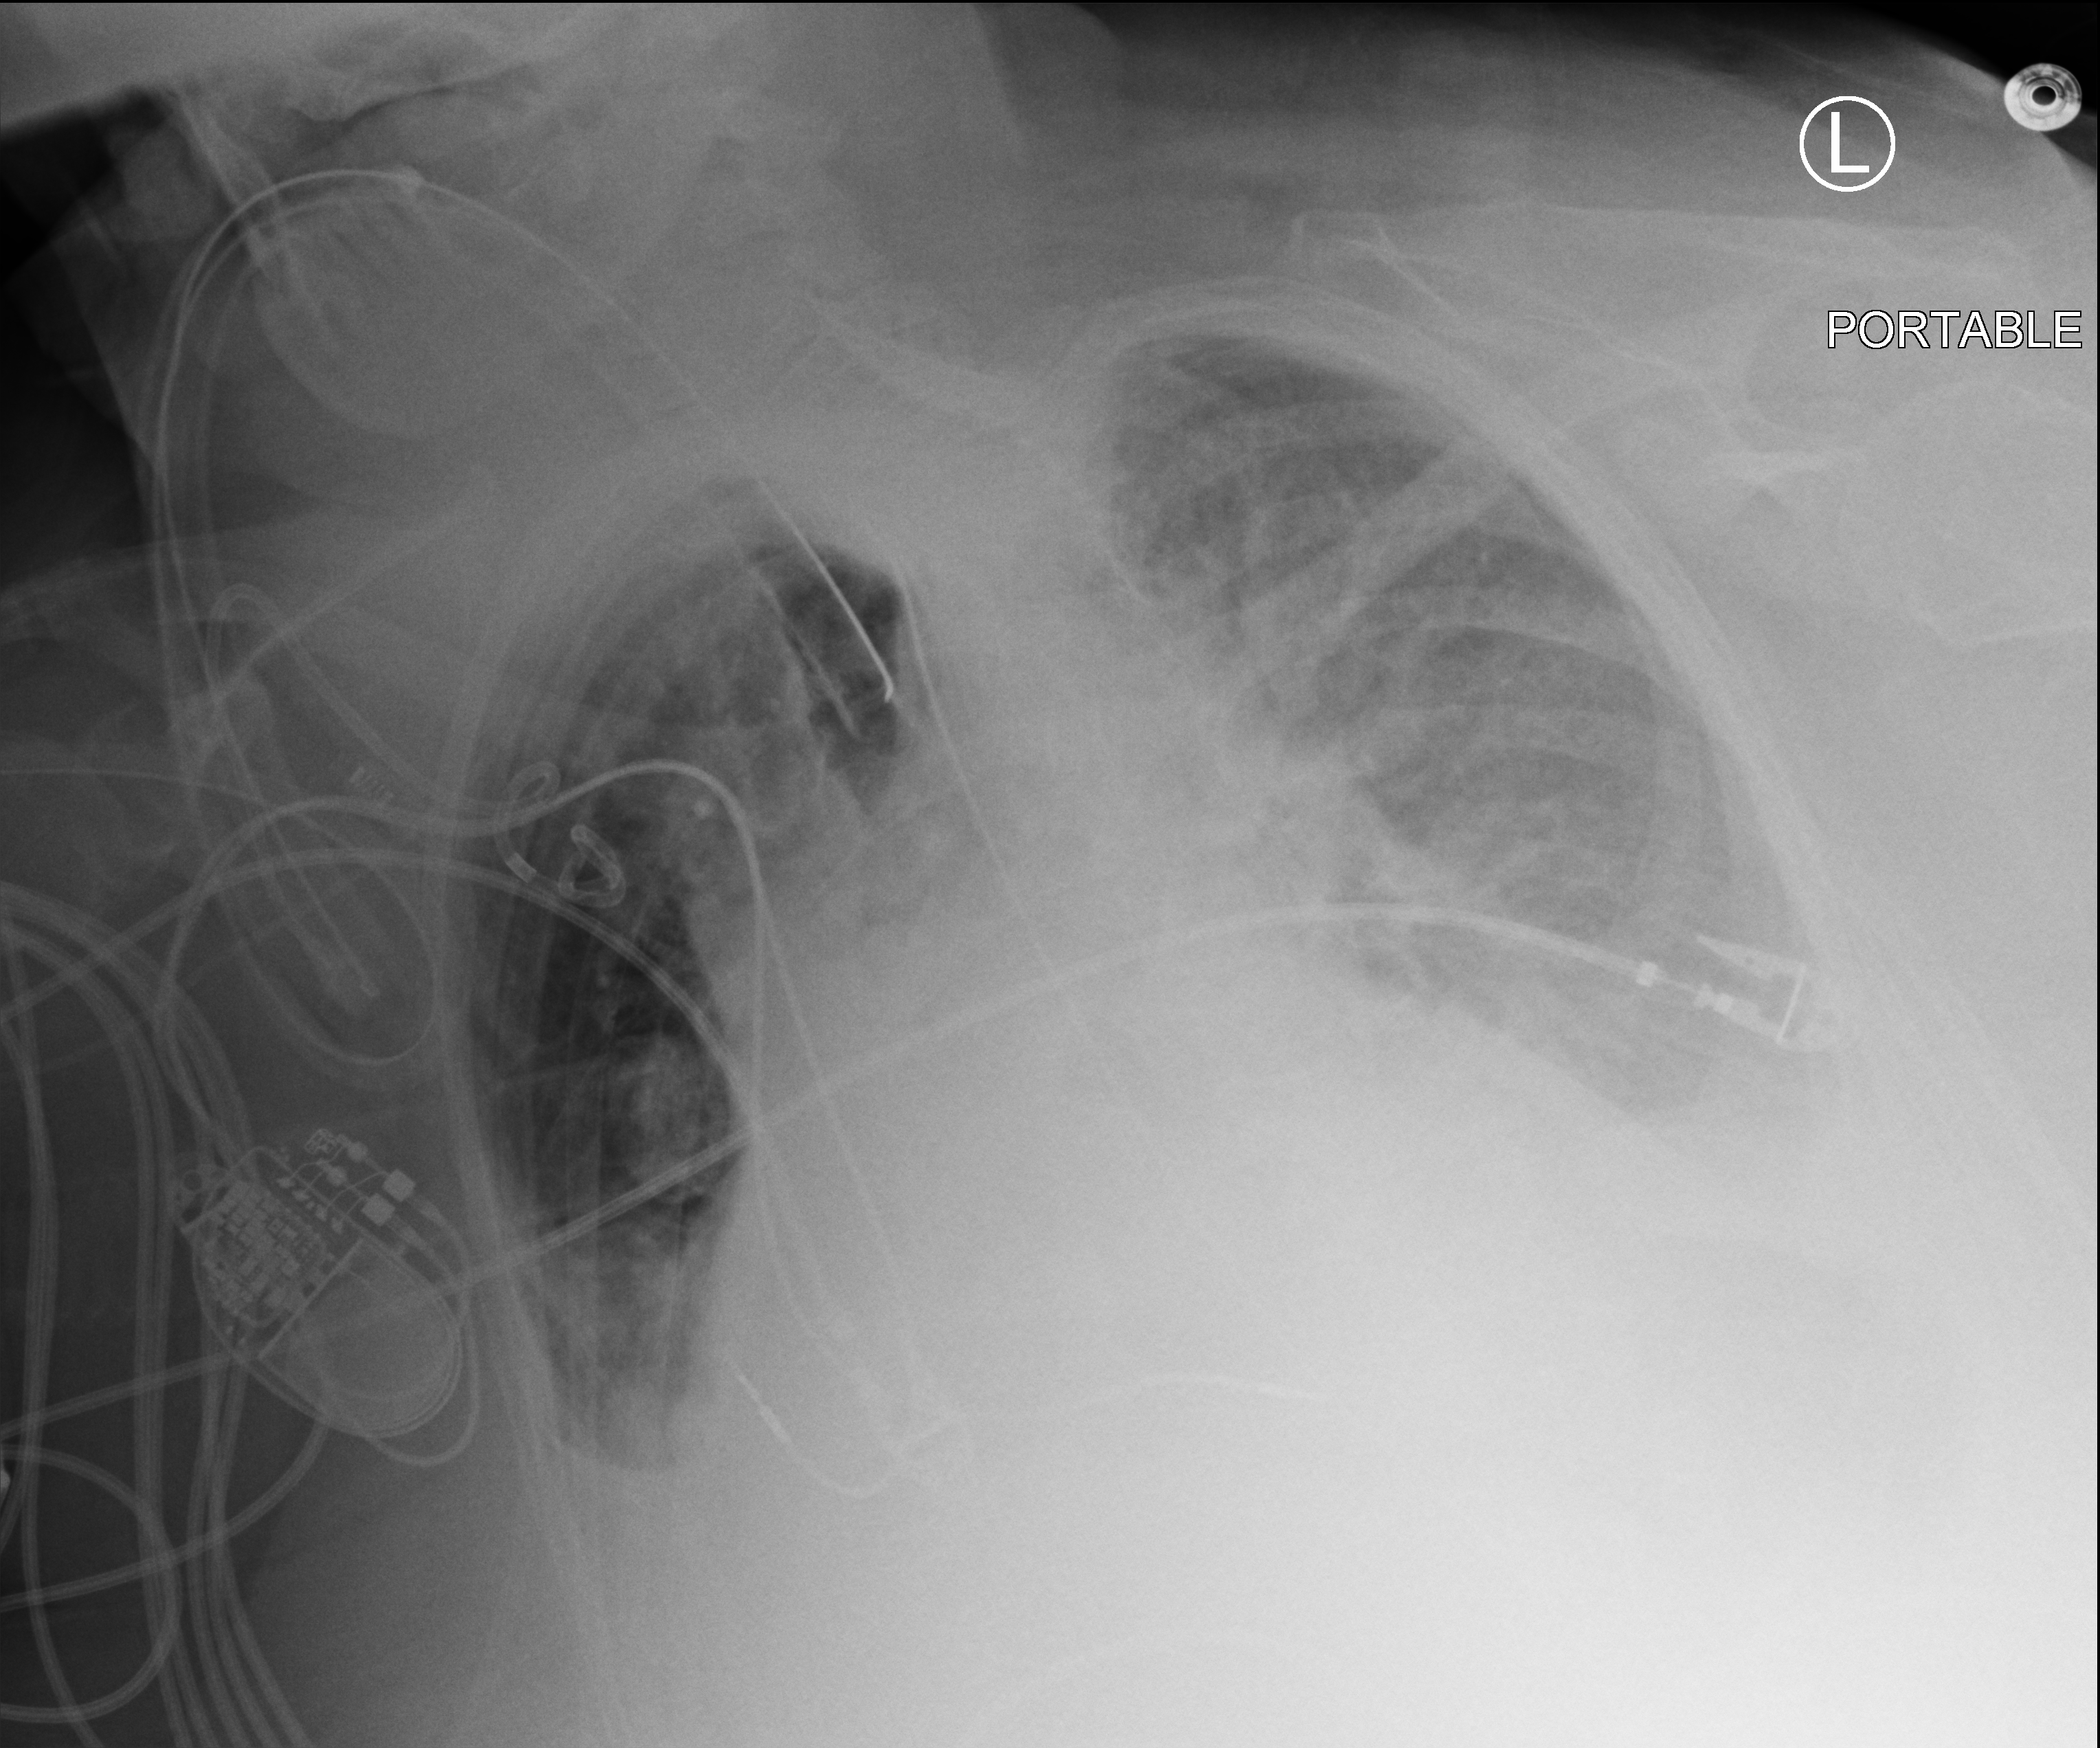
Bedside chest radiograph (computed radiography); anteroposterior (AP) projection. Patient hospitalised with COVID-19; female, aged 75–90 years.
Hospital-stay facts (about this admission, not read from this image; timing relative to this image not recorded): hypertension (admission record): yes; smoking status (admission record): former.